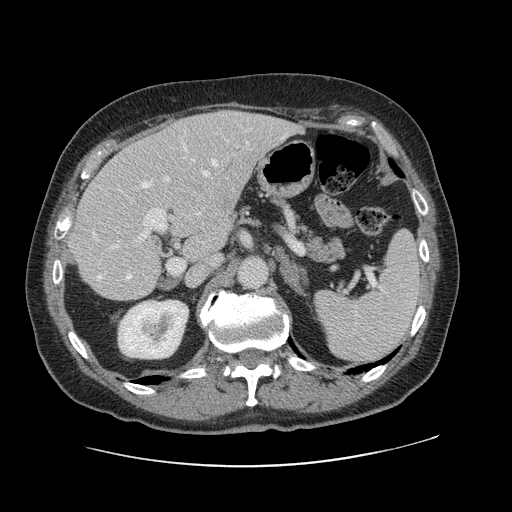
Contrast-enhanced abdominal CT, one axial slice; position 69 of 138 along the scan axis; 120 kVp; intravenous contrast given; soft-tissue window (W 400 / L 40 HU); 2.5 mm slice thickness; 512 × 512 image matrix, field of view 402 × 402 mm. Male patient, age 71 years. Case-level facts recorded for this patient, not image findings: diagnosis: colorectal cancer liver metastases, imaged before liver resection; multiple liver metastases: no; largest metastasis: 3.3 cm.
Annotated regions visible in this slice (expert manual segmentation):
- hepatic veins: box from (x=92, y=146) to (x=223, y=281) px
- liver: (x=72, y=112)–(x=295, y=300)
- planned liver remnant (the part of the liver to remain after resection): (x=71, y=145)–(x=224, y=300)
- portal vein (with intrahepatic branches): (x=110, y=142)–(x=248, y=274)
- liver metastasis: (x=217, y=191)–(x=234, y=208)